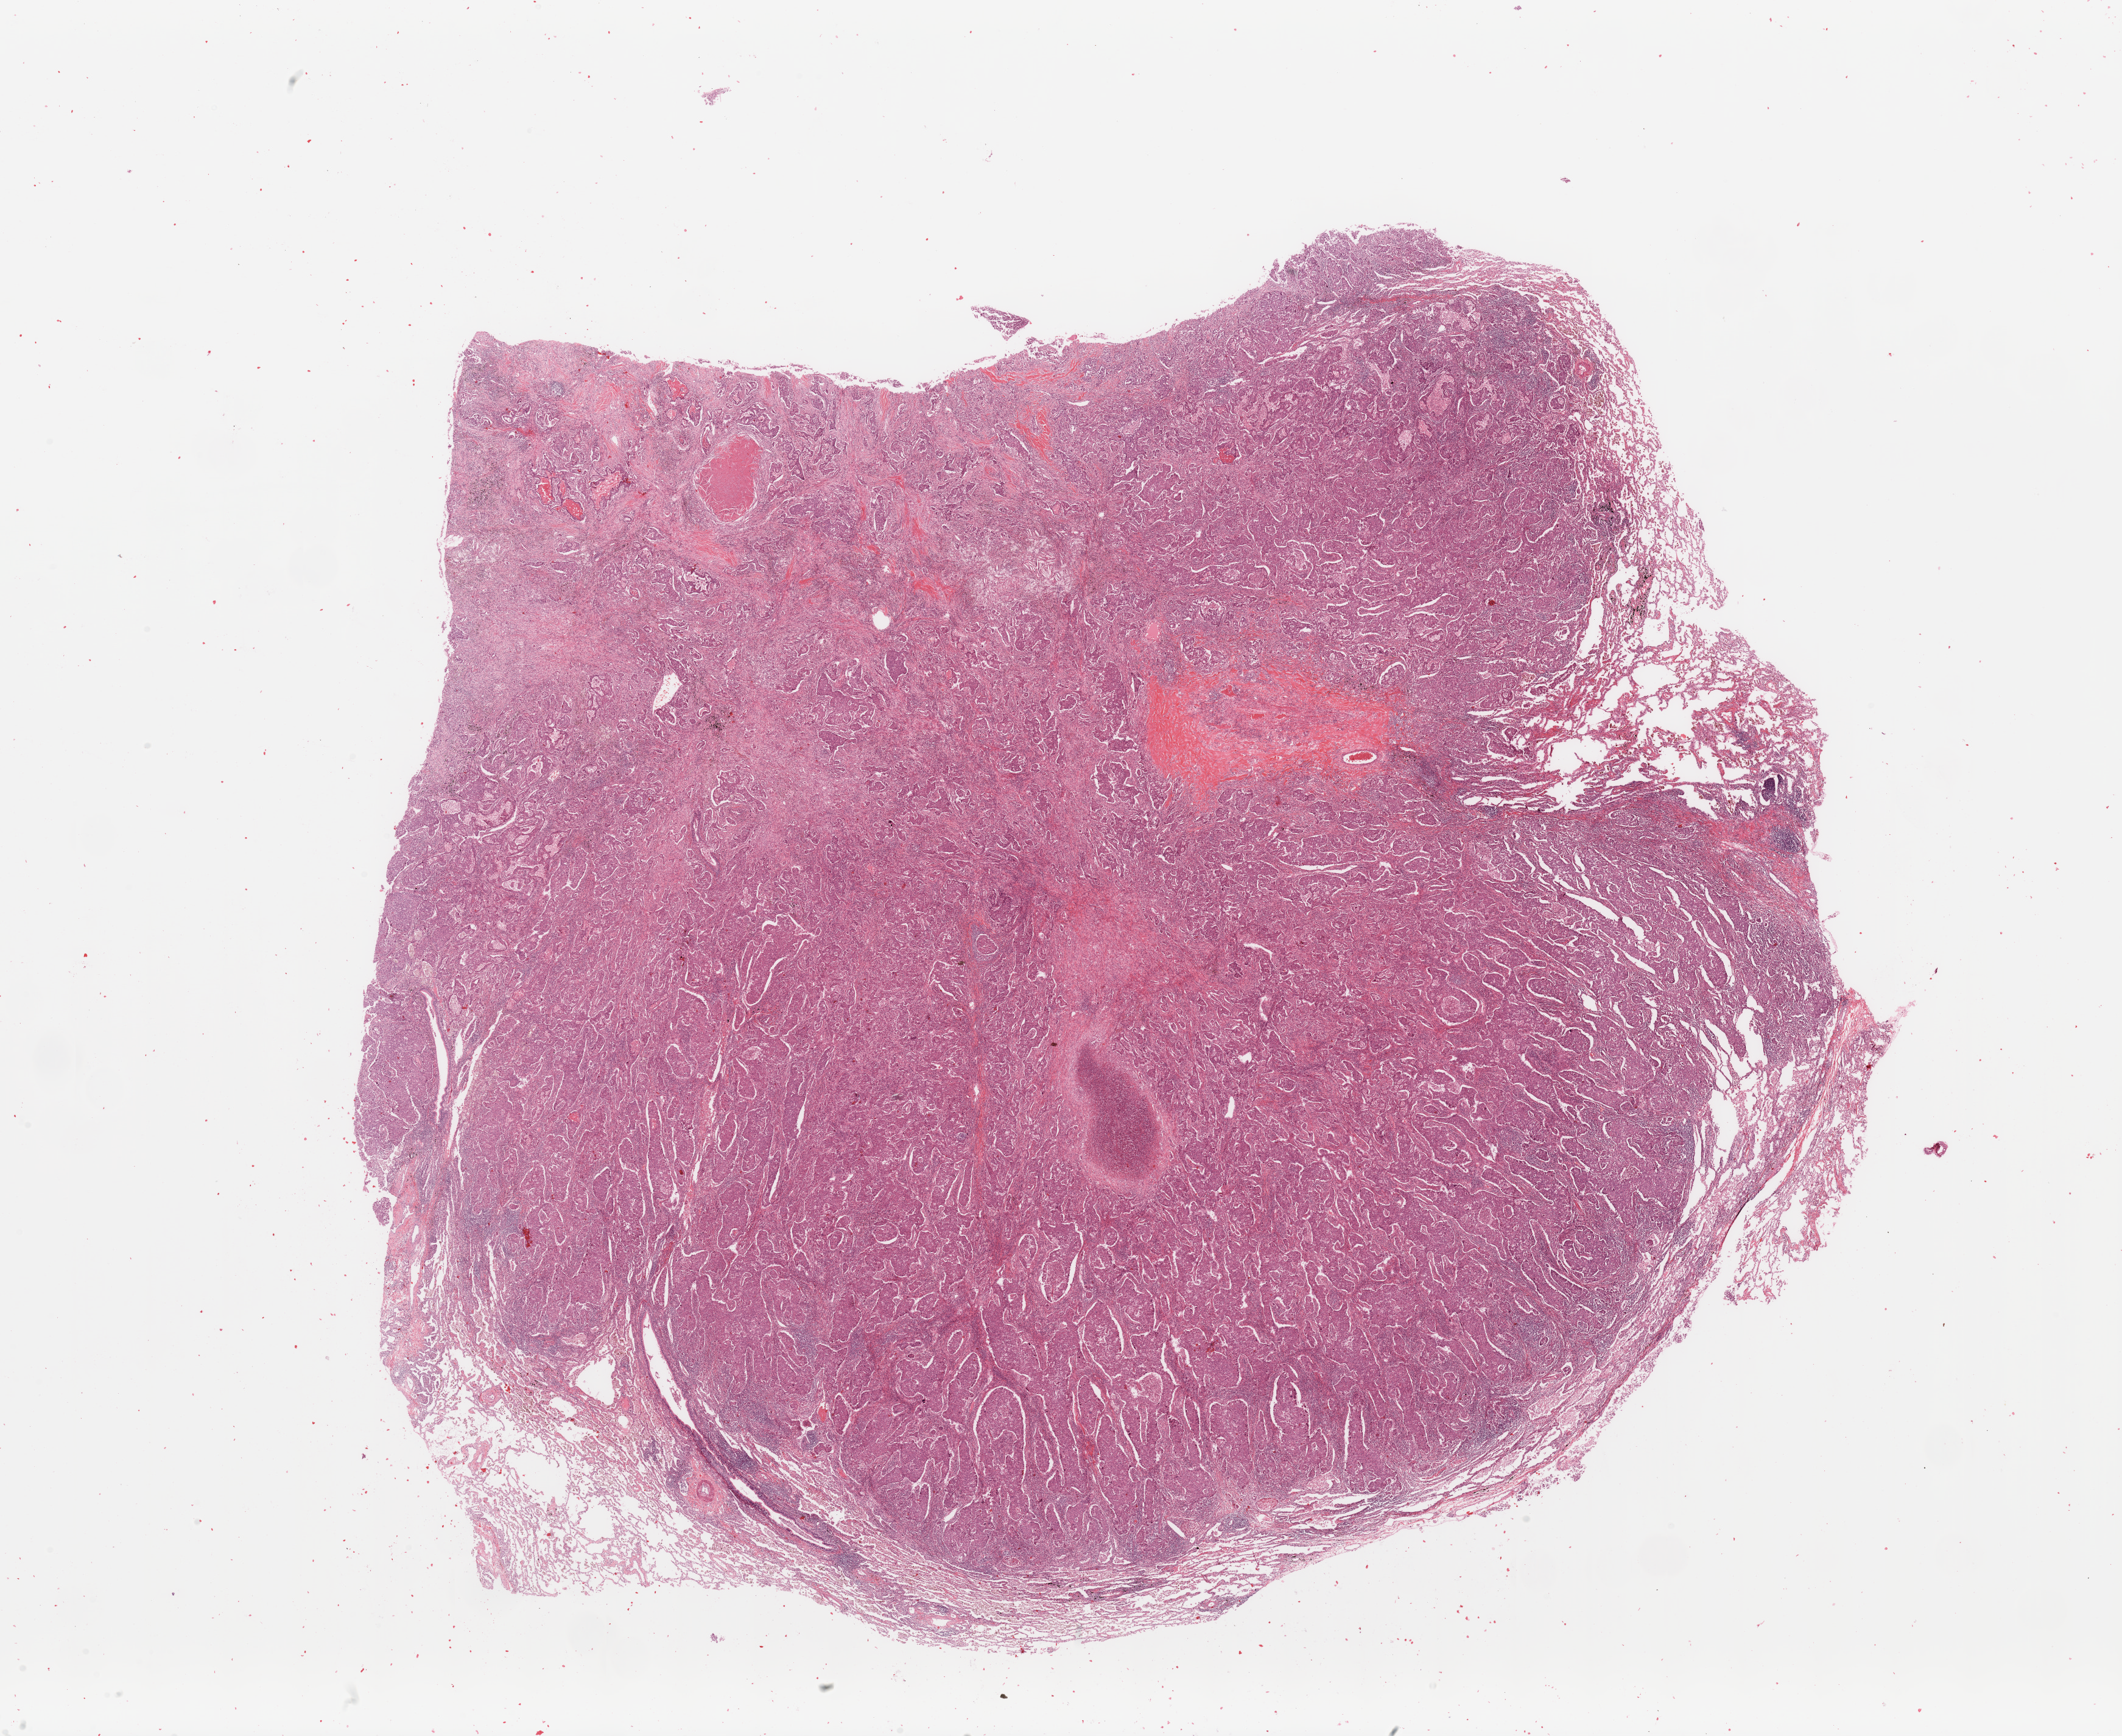
Whole-slide histology image, H&E-stained — a low-resolution overview of the entire scanned area, about 27.6 x 22.5 mm (slide scanned at 20x); lung, tumour tissue. 49-year-old male patient.
Histologic diagnosis: Adenocarcinoma, NOS.